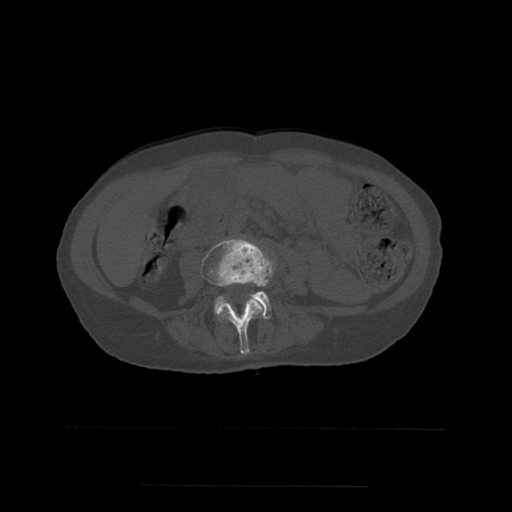
CT including the spine, one axial slice. Position 180 of 544 along the scan axis. Bone window (W 1800 / L 400 HU). 1.25 mm slice thickness. 512 × 512 image matrix, field of view 350 × 350 mm. Patient age 58 years. From the clinical record (not read from this slice): primary cancer: lung.
Outlined on this slice (semi-automatically segmented with operator editing):
- L3 vertebra: bounding box (x1, y1, x2, y2) in pixels: (202, 239, 273, 355)
- L4 vertebra: (215, 266, 273, 319)